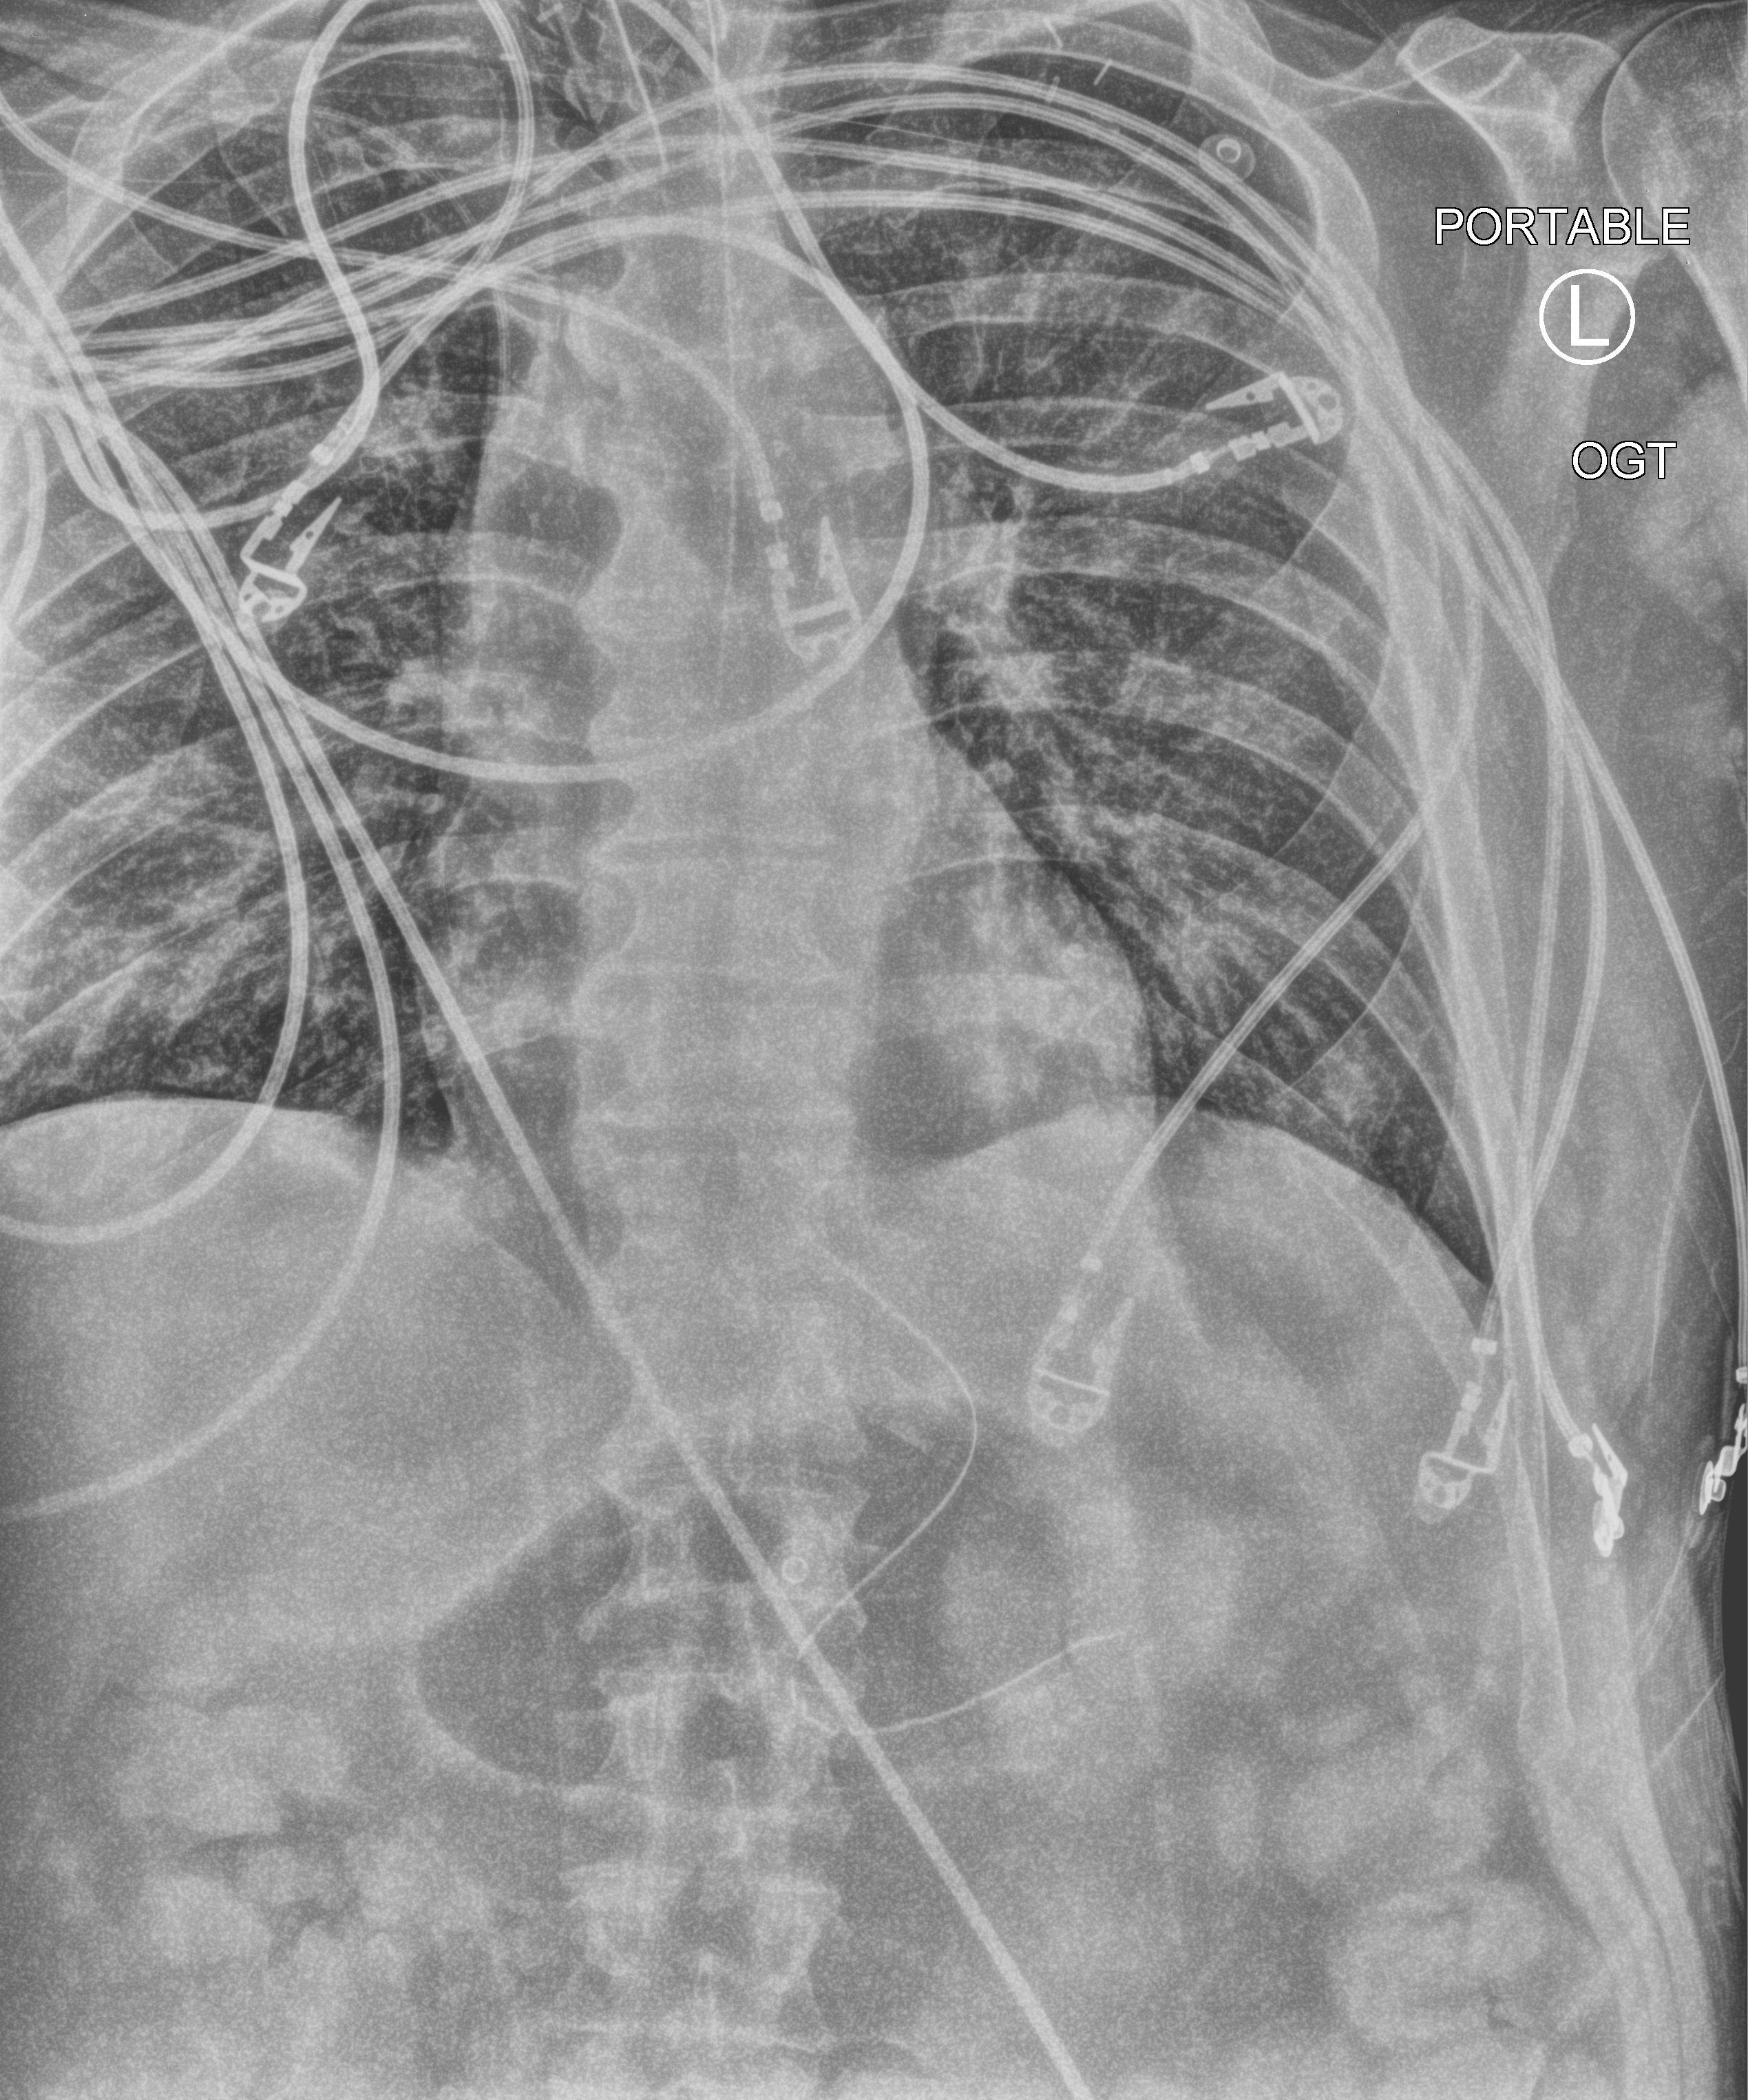
Bedside chest radiograph (computed radiography), anteroposterior (AP) projection. Adult patient hospitalised with COVID-19, age 18–59 years.
From the hospital-stay record, not from the radiograph (when in the stay this image was taken is not recorded):
- chronic kidney disease (admission record): yes